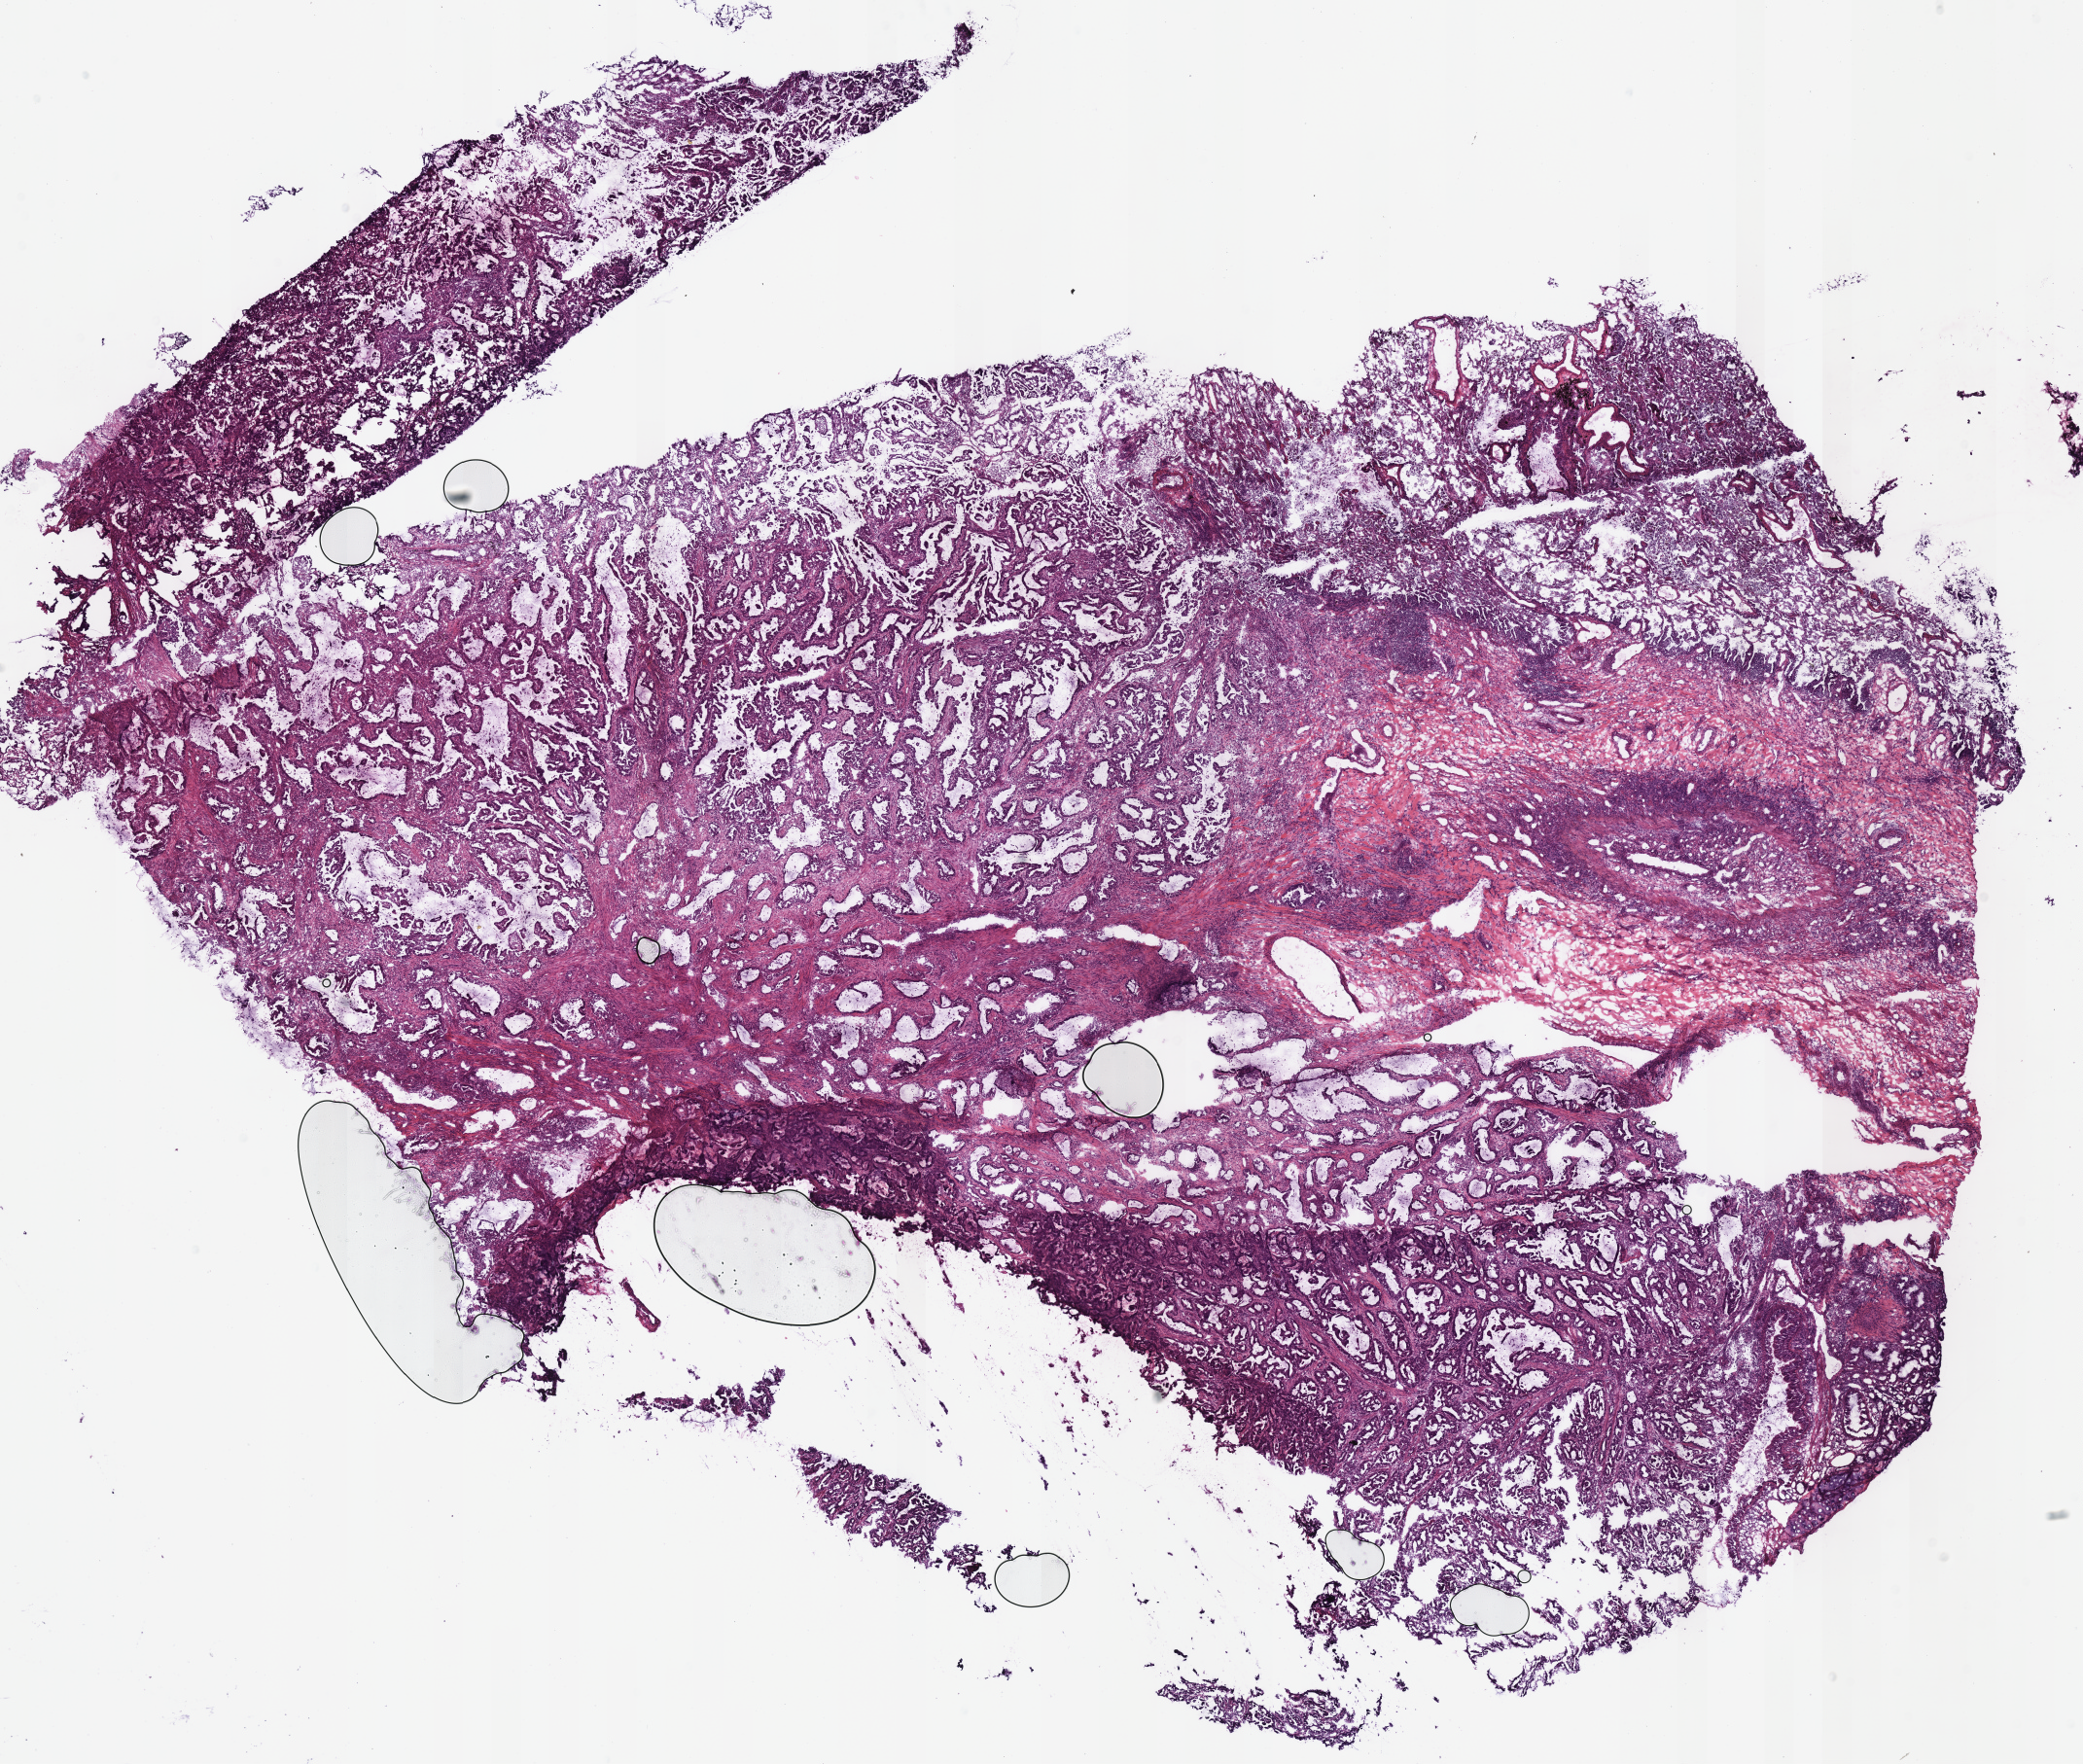
Digitized H&E tissue section (whole slide), a low-resolution overview of the entire scanned area, about 16.9 x 14.3 mm (from a 40x scan). Frozen section. Lung, primary tumour sample. Male, age 50 years at initial diagnosis. Slide review estimates, as recorded: tumour cells 85%, tumour nuclei 70%, normal cells 5%, stromal cells 10%, necrosis 0%. Infiltration values recorded for this section: lymphocyte infiltration 10%, monocyte infiltration 0%, neutrophil infiltration 15%.
* AJCC pathologic stage: IIA (7th edition)
* histologic diagnosis: Papillary adenocarcinoma, NOS (middle lobe, lung)